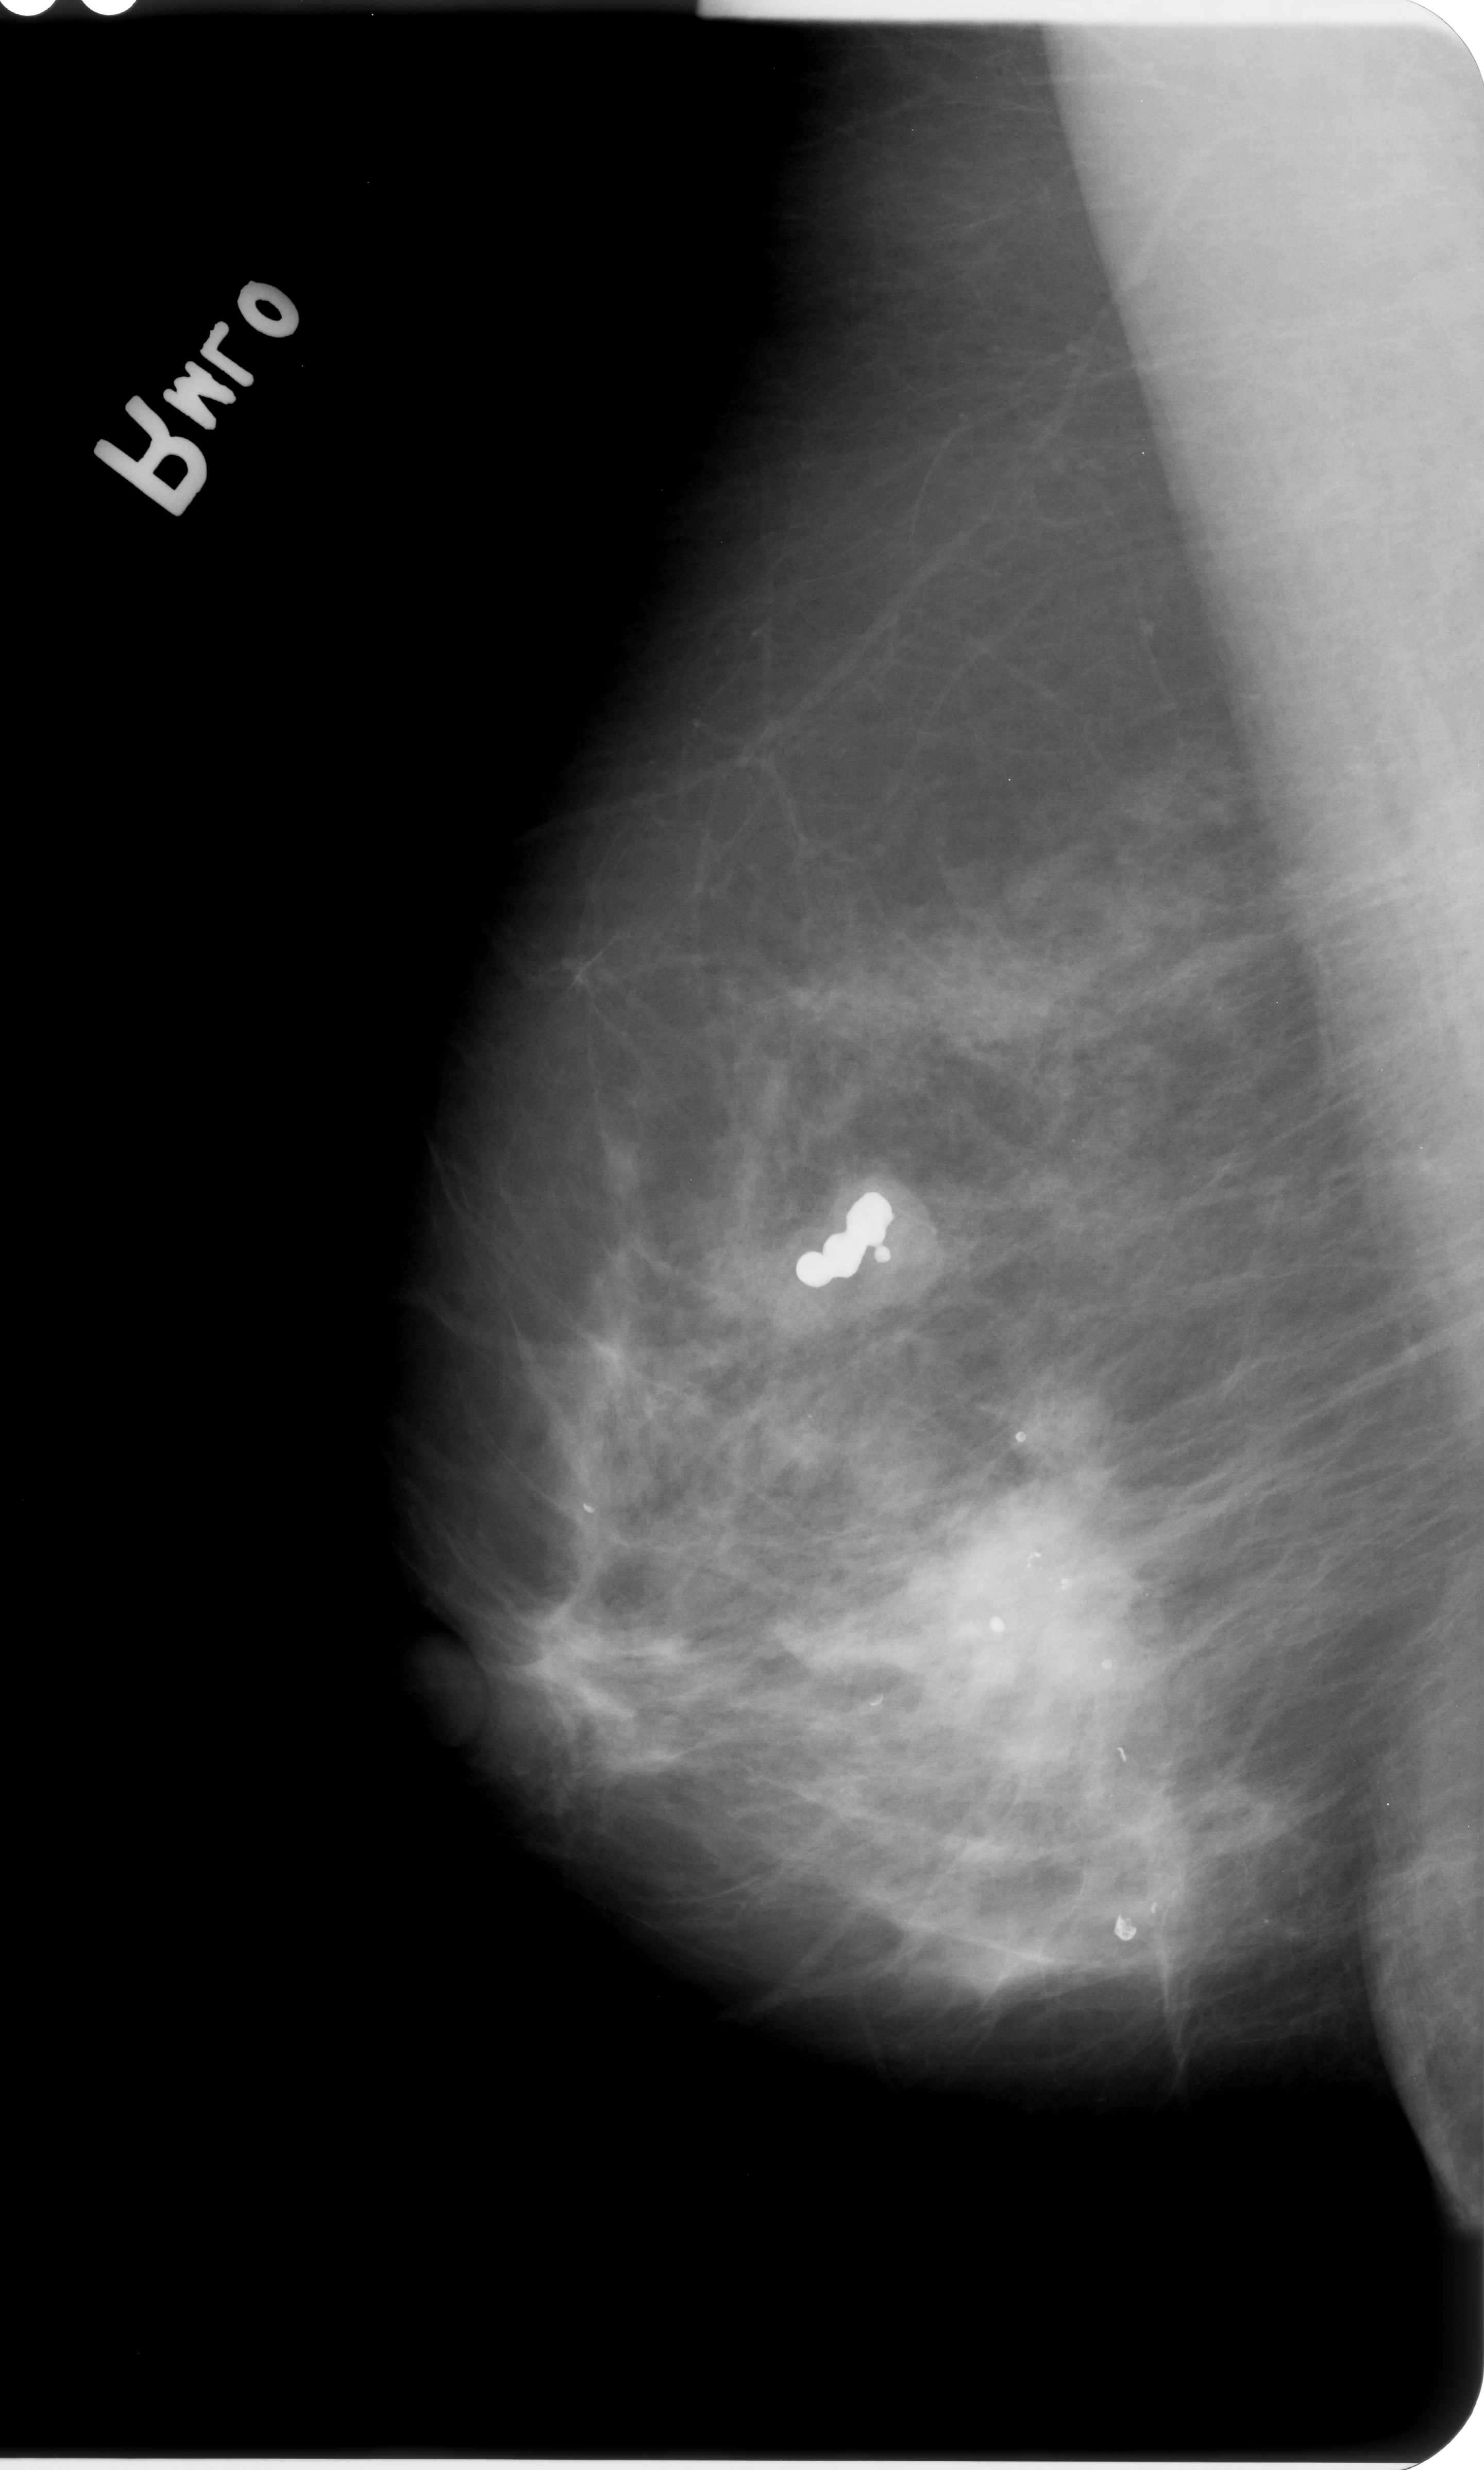
Scanned film-screen mammogram, right breast, MLO view.
- Abnormality record for this image: Finding 1 of 2: calcifications, morphology pleomorphic, distribution clustered; BI-RADS assessment category 4; pathology (as recorded): malignant.
- Finding 2 of 2: calcifications, morphology pleomorphic, distribution clustered; BI-RADS assessment category 4; subtlety rating 4 on a 1 (subtle) to 5 (obvious) scale; pathology result (as recorded, not read from the image): malignant.